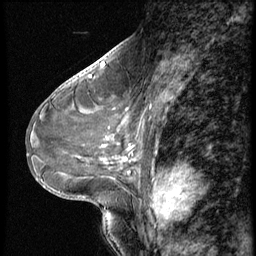
Breast MRI (dynamic contrast-enhanced), one sagittal slice. Slice 29 of 56 in the series (ordered by position). Dynamic contrast-enhanced series, image 2 of 3 at this slice position (ordered by acquisition). 1.5 T. TE 4.2 ms, TR 9 ms. 256 × 256 image matrix, field of view 180 × 180 mm. Patient: female, 46 years. From the clinical record (not read from this slice): setting: breast cancer imaged before/during neoadjuvant chemotherapy; receptor status: HER2-positive.
Outlined on this slice (semi-automatic segmentation, software-assisted and operator-edited):
- analysis volume of interest (the breast-tissue region the enhancement analysis was run in; not a lesion): bounding box [x1, y1, x2, y2] px = [64, 98, 174, 182]
- tumour enhancement mask (voxels above the 140 % enhancement threshold inside the analysis volume of interest): [124, 156, 174, 182]